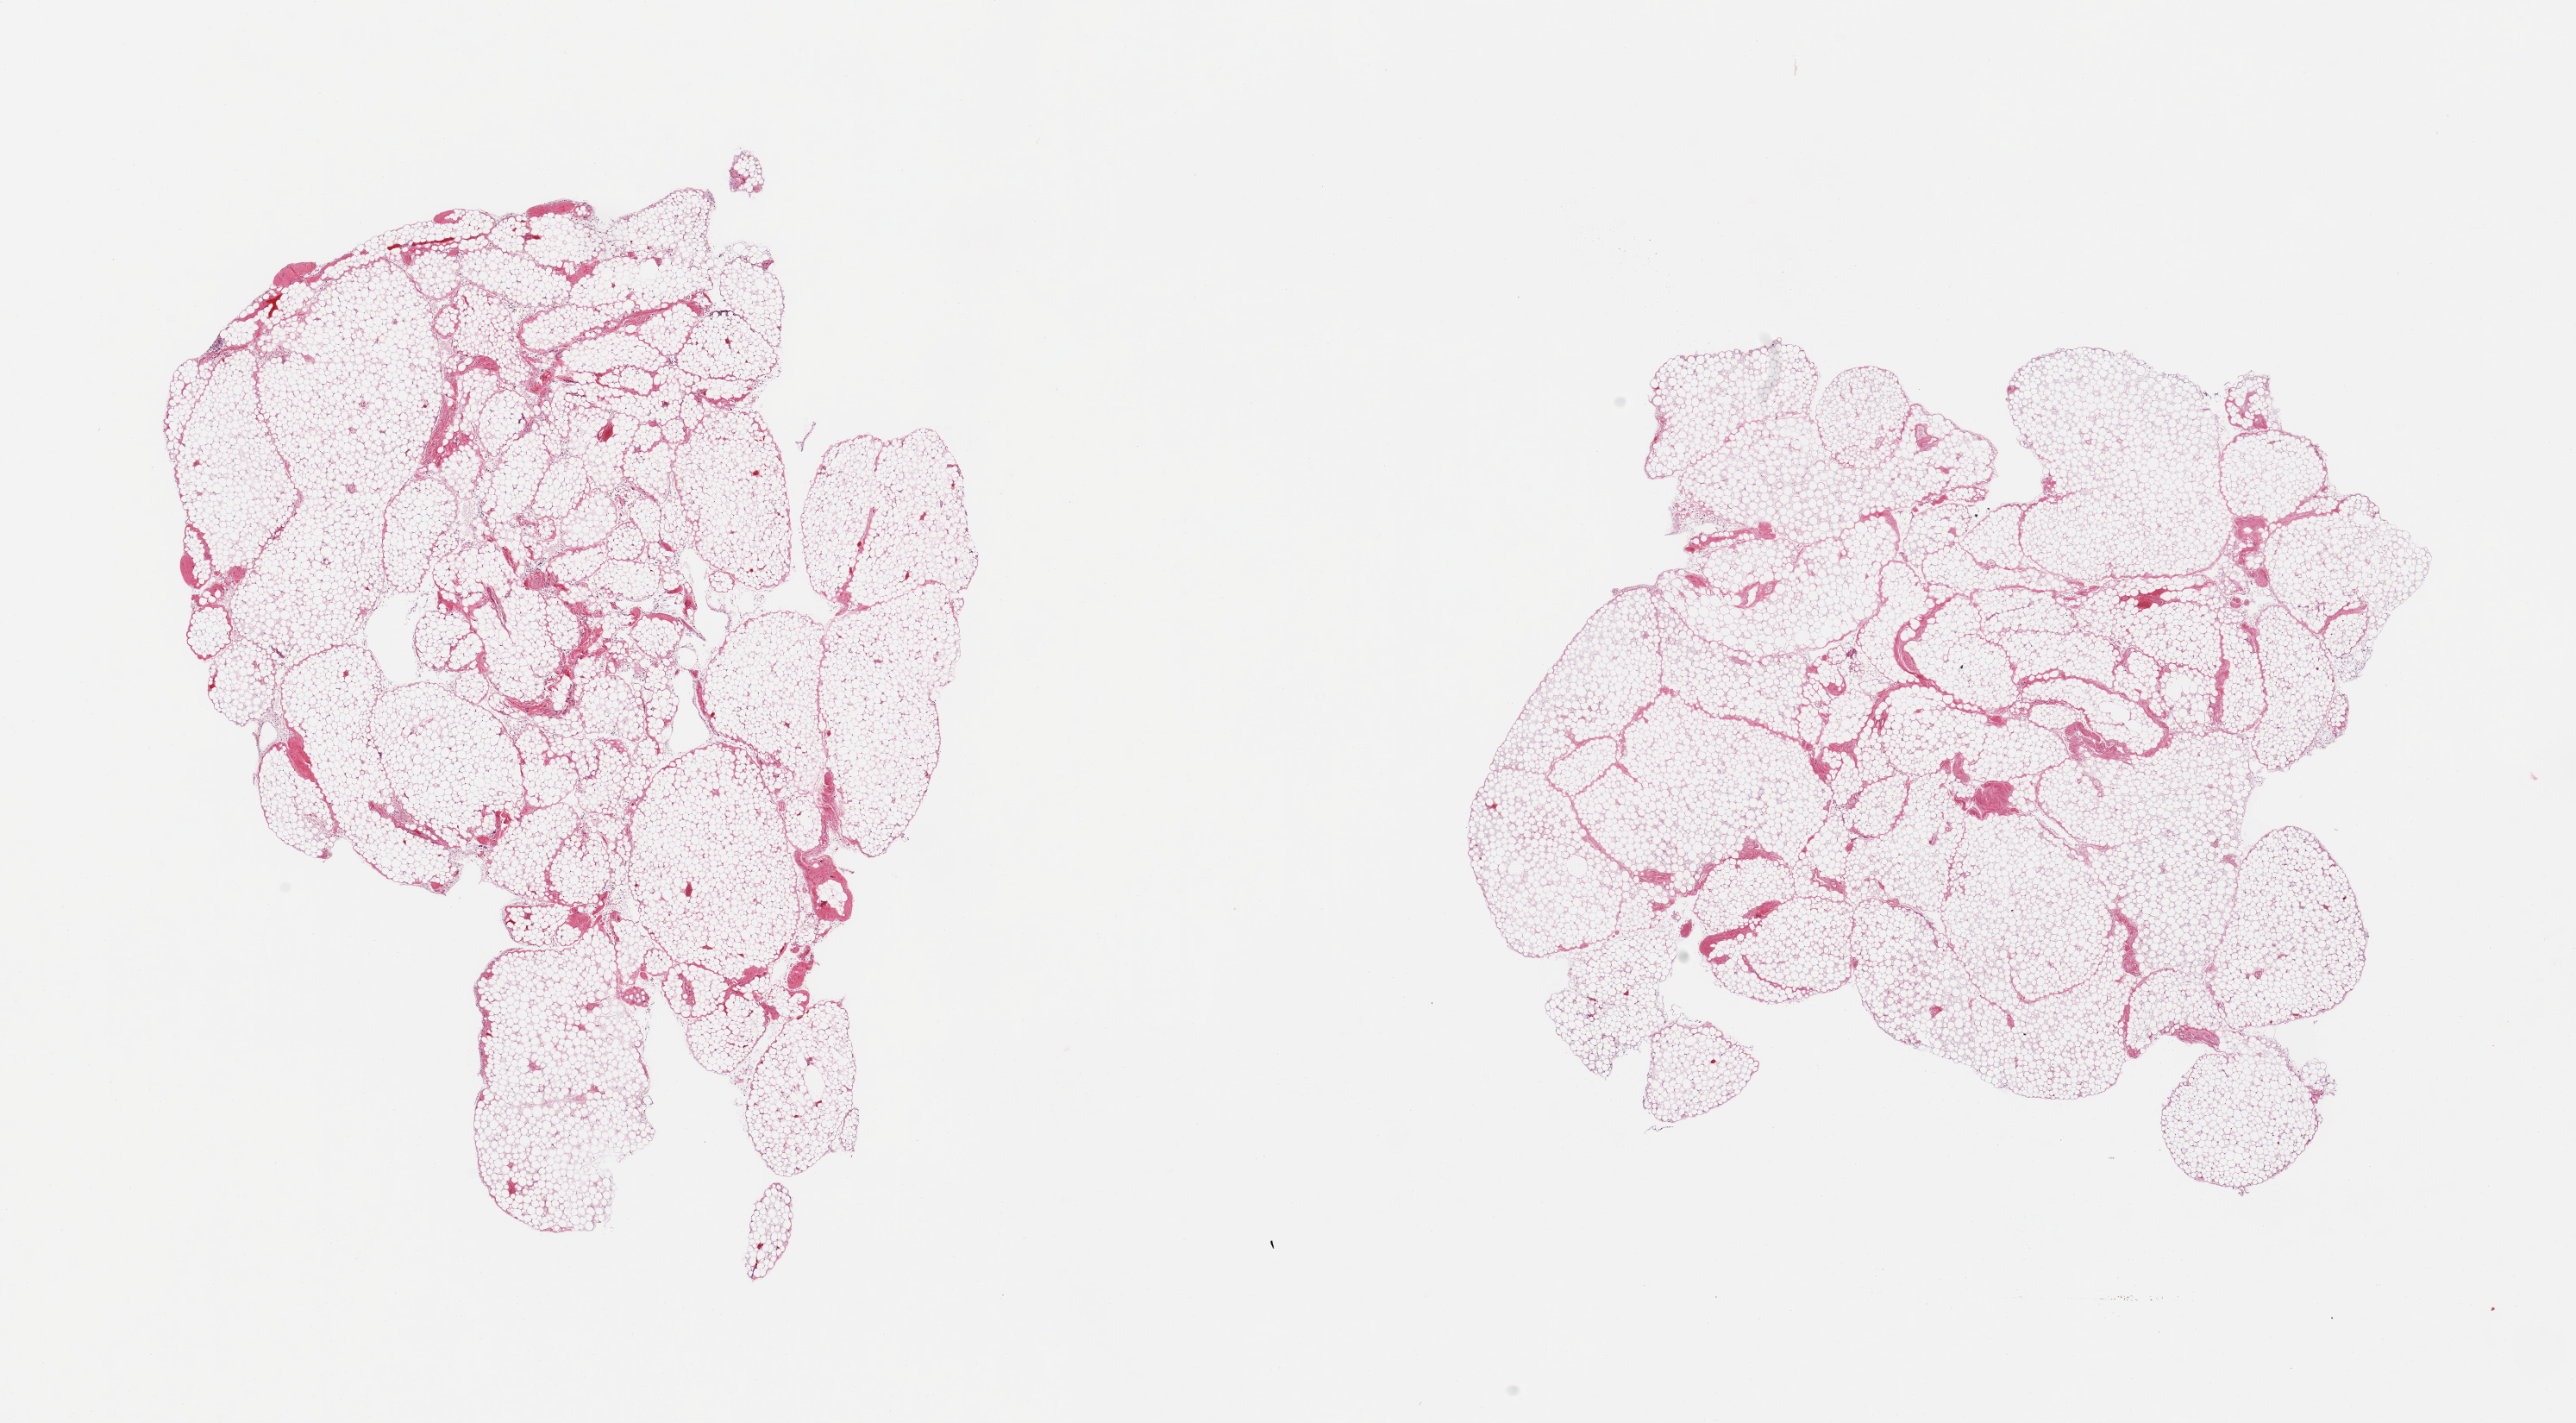
Digitized hematoxylin and eosin (H&E)-stained section, brightfield, a low-resolution overview of the entire scanned area, about 23.6 x 13.1 mm (slide scanned at 20x). PAXgene-fixed paraffin-embedded (PFPE) section. Section of omentum (target tissue). Tissue donor sample. Donor: male.
Reviewer comment on this tissue sample: 2 pieces, ~5-10% fascia/vascular elements.